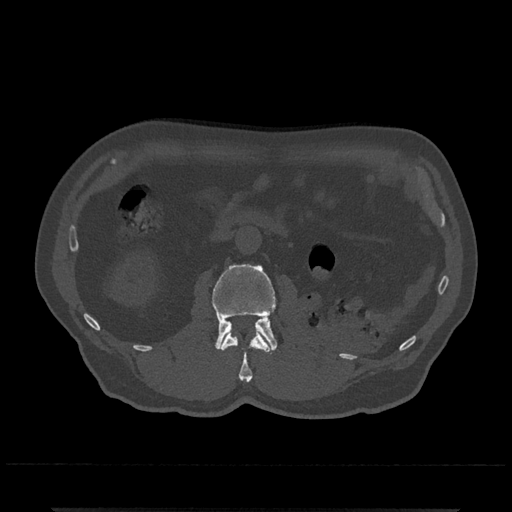
CT including the spine, one axial slice; position 316 of 797 along the scan axis; reconstruction kernel Br40s/3; 120 kVp; bone window (W 1800 / L 400 HU); 512 × 512 image matrix, field of view 393 × 393 mm. Male patient, age 67 years. From the clinical record (not read from this slice): primary cancer: prostate.
Outlined on this slice (semi-automatic segmentation, software-assisted and operator-edited):
- L1 vertebra: bounding box <221,329,270,382> (left, top, right, bottom; pixels)
- L2 vertebra: <212,264,278,353>